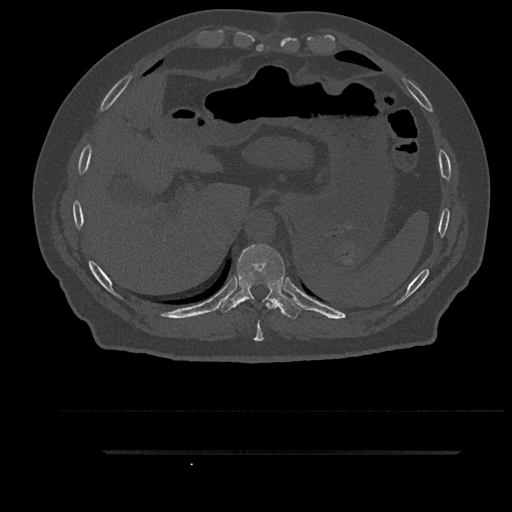
CT including the spine, one axial slice. Slice 386 of 797 in the series (ordered by position). Bone window (W 1800 / L 400 HU). 512 × 512 image matrix, field of view 432 × 432 mm. Male patient, age 63 years. Case-level facts recorded for this patient, not image findings: primary cancer: renal; vertebrae with lytic lesions (as recorded): T8.
Structures marked on this image (semi-automatic segmentation, software-assisted and operator-edited):
- T10 vertebra: bounding box <219,244,302,319> (left, top, right, bottom; pixels)
- T9 vertebra: <254,299,277,341>